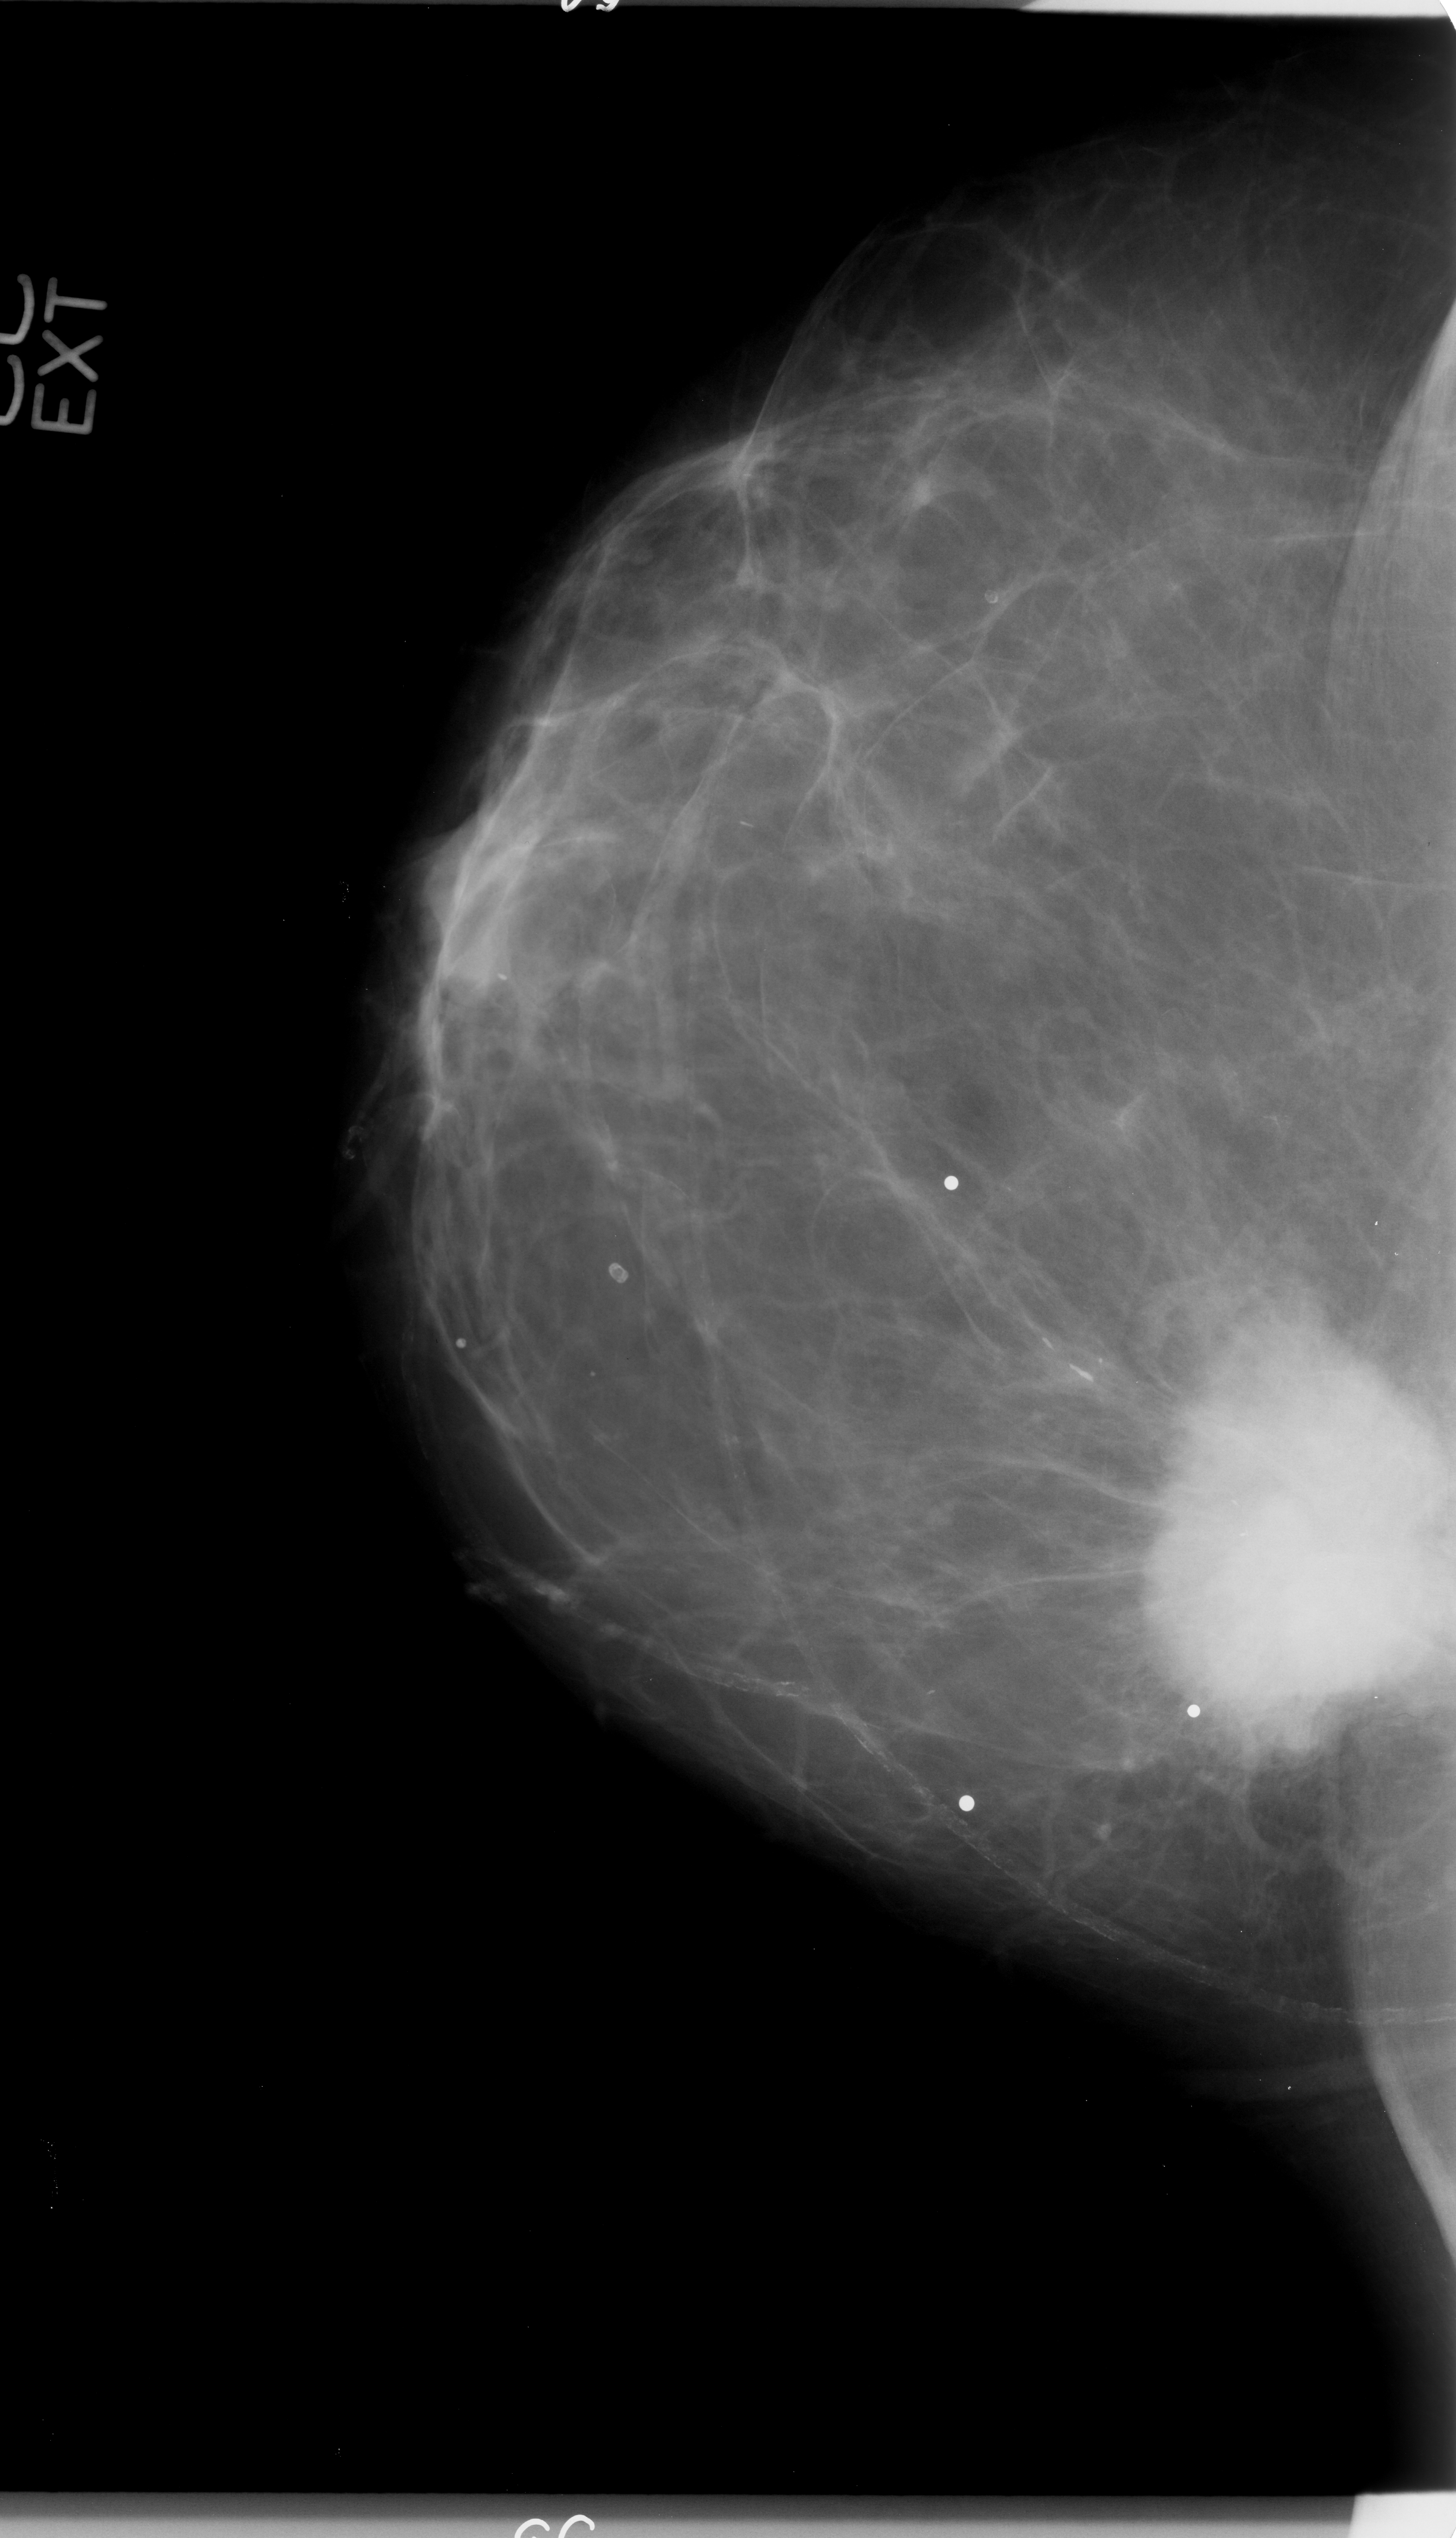
Mammogram (digitized film); right breast; craniocaudal (CC) view.
- Abnormality record for this image: mass, shape irregular / architectural distortion, margins spiculated; BI-RADS assessment category 4; subtlety rating 5 on a 1 (subtle) to 5 (obvious) scale; pathology result (as recorded, not read from the image): malignant.